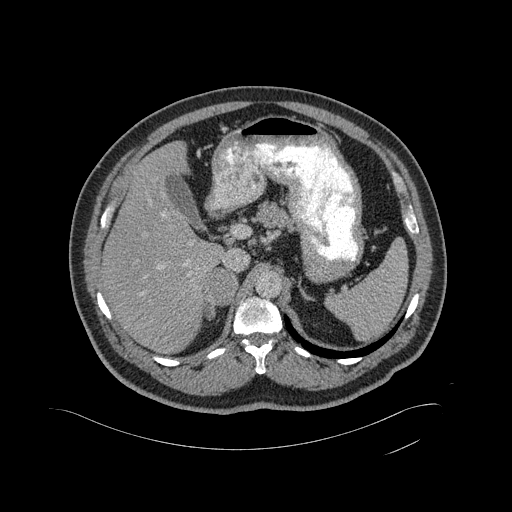
Contrast-enhanced abdominal CT, one axial slice. 120 kVp. Intravenous contrast given. Soft-tissue window (W 400 / L 40 HU). 512 × 512 image matrix. Patient: male, 56 years. From the clinical record (not read from this slice): diagnosis: adrenocortical carcinoma; tumour side: right adrenal; tumour size at pathology: 11.6 cm; Ki-67 index: 50 %; stage (as recorded): 3.
Structures marked on this image (semi-automatically segmented with operator editing):
- mass: box from (x=204, y=268) to (x=236, y=304) px